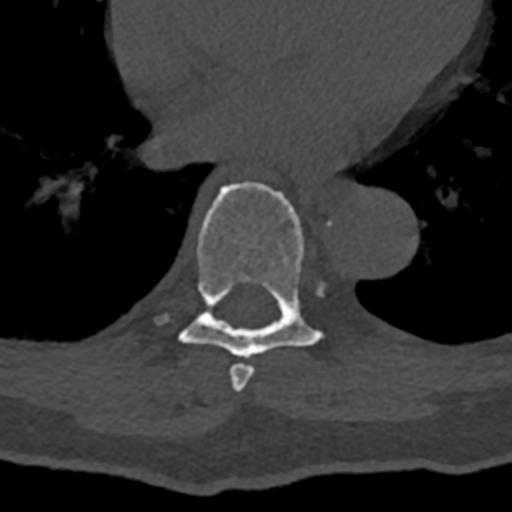
CT including the spine, one axial slice. Slice 712 of 797 in the series (ordered by position). Reconstruction kernel Br40s/3. Bone window (W 1800 / L 400 HU). 512 × 512 image matrix, field of view 160 × 160 mm. Patient: male, 74 years. Case-level facts recorded for this patient, not image findings: primary cancer: renal.
Annotated regions visible in this slice (semi-automatic segmentation, software-assisted and operator-edited):
- T7 vertebra: bounding box [x1, y1, x2, y2] px = [229, 364, 254, 391]
- T8 vertebra: [157, 181, 330, 358]